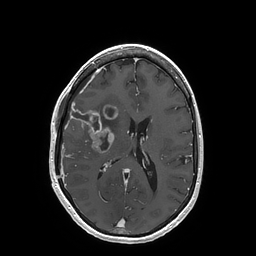
Brain MRI from a brain-tumour surgery series, one axial slice; position 74 of 202 along the scan axis; T1-weighted post-contrast; 1 mm slice thickness; 256 × 256 image matrix, field of view 250 × 250 mm. Case-level facts recorded for this patient, not image findings: histopathology: Glioblastoma; WHO grade: 4.
Outlined on this slice (manually delineated by an expert):
- tumour: box from (x=69, y=106) to (x=117, y=153) px